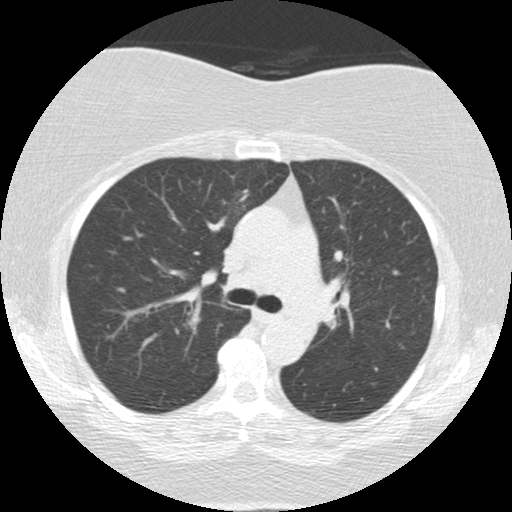
Low-dose screening chest CT, one axial slice. Position 87 of 136 along the scan axis. 120 kVp. Lung window (W 1500 / L -600 HU). 2.5 mm slice thickness. 512 × 512 image matrix, field of view 309 × 309 mm.
Annotated regions visible in this slice (expert manual segmentation):
- lesion 2 (tumor, mediastinum): bounding box <300,285,333,325> (left, top, right, bottom; pixels)